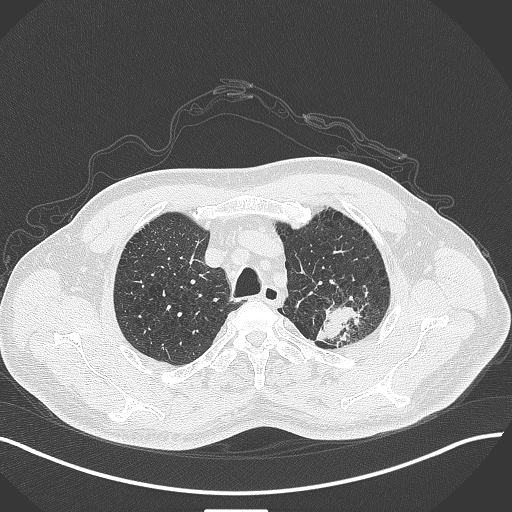
Chest CT, one axial slice. Position 349 of 429 along the scan axis. Reconstruction kernel B70f. 120 kVp. Lung window (W 1500 / L -600 HU). 512 × 512 image matrix. Patient: male, 55 years. From the clinical record (not read from this slice): clinical TNM (as recorded): T3 N0 M1c; histopathological grade: G3.
Structures marked on this image (bounding box drawn by a radiologist):
- lung tumour (recorded histology: adenocarcinoma): bounding box <308,289,365,349> (left, top, right, bottom; pixels)